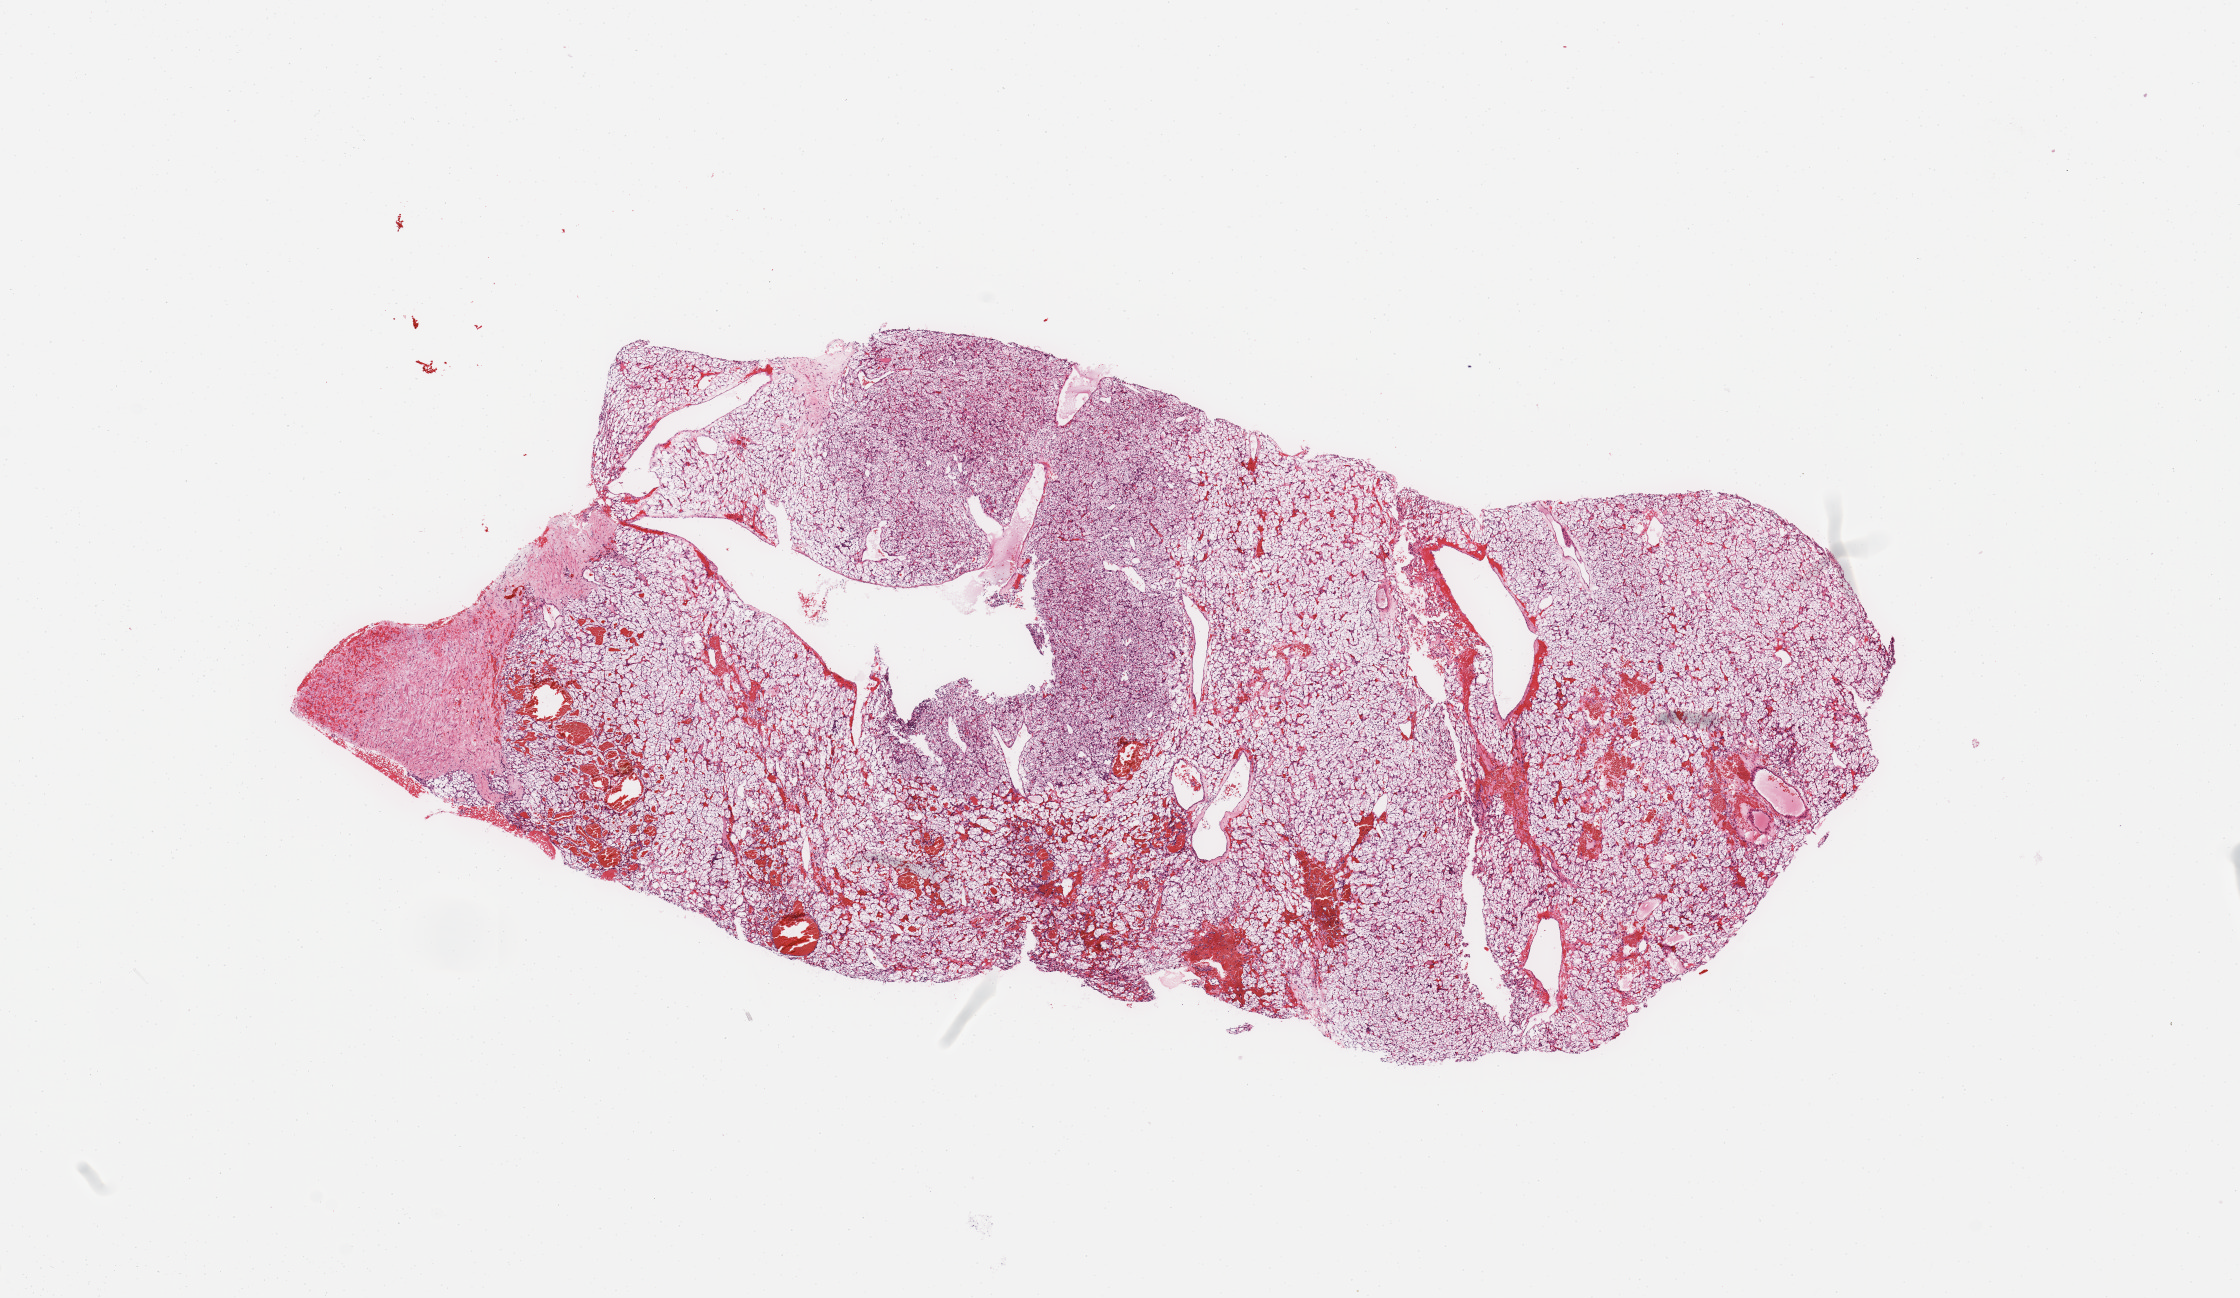
Digitized H&E tissue section (whole slide), whole scanned area (about 17.7 x 10.3 mm, slide scanned at 20x) shown as a low-resolution overview, tumour tissue sample, sampled site: kidney. Female, 56 y/o. Histologic grade: G2 (moderately differentiated). Composition of this section per pathologist review: tumour nuclei 90%, necrosis 0%.
• diagnosis: Renal cell carcinoma, NOS
• AJCC pathologic stage: III